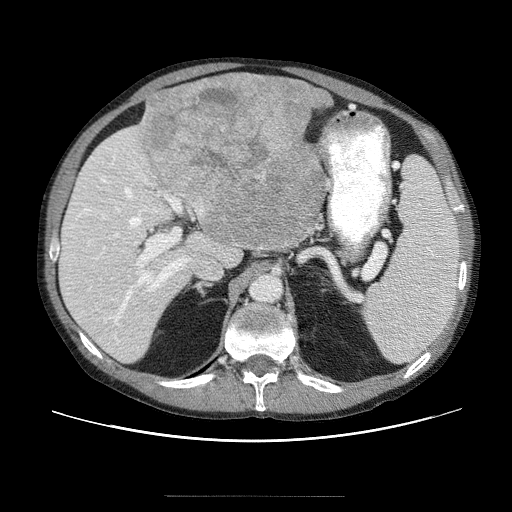
Contrast-enhanced abdominal CT (liver protocol), one axial slice. Slice 29 of 69 in the series (ordered by position). Soft-tissue window (W 400 / L 40 HU). 2.5 mm slice thickness. 512 × 512 image matrix, field of view 380 × 380 mm. From the clinical record (not read from this slice): diagnosis: hepatocellular carcinoma (patient treated with transarterial chemoembolisation; whether this scan precedes or follows treatment is not stated here); TNM stage (as recorded): Stage-IVB; Child-Pugh class: B; tumour differentiation: poorly differentiated; tumour nodularity: multinodular.
Structures marked on this image (semi-automatic segmentation, software-assisted and operator-edited):
- liver parenchyma outside the tumour (the mass and vessels are separate outlines, so this box may not span the whole liver): bounding box [x1, y1, x2, y2] px = [58, 78, 324, 362]
- mass: [134, 75, 334, 255]
- liver vessels: [70, 149, 229, 350]